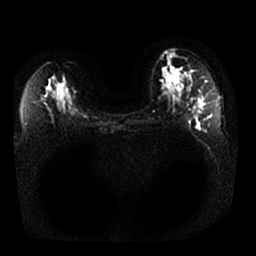
Breast MRI, one axial slice; slice 17 of 25 in the series (ordered by position); diffusion-weighted series; image 2 of 4 stored at this slice position (different b-values; order by instance number); 1.5 T; 4 mm slice thickness; 256 × 256 image matrix. Female patient.
Structures marked on this image (outlined manually by an expert reader):
- tumour on diffusion-weighted imaging: bounding box <198,99,204,105> (left, top, right, bottom; pixels)